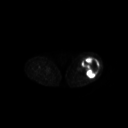
FDG PET of an extremity soft-tissue mass (from a PET/CT study), one axial slice; 3.27 mm slice thickness; 128 × 128 image matrix, field of view 700 × 700 mm. Female patient, age 62 years. From the clinical record (not read from this slice): histological type: undifferentiated – high grade; grade: high; site of the primary tumour: left thigh.
Structures marked on this image (expert contour drawn on MRI and transferred to this co-registered scan by the dataset authors):
- gross tumour volume including surrounding oedema: box from (x=82, y=57) to (x=100, y=78) px
- gross tumour volume (mass): (x=82, y=57)–(x=100, y=78)